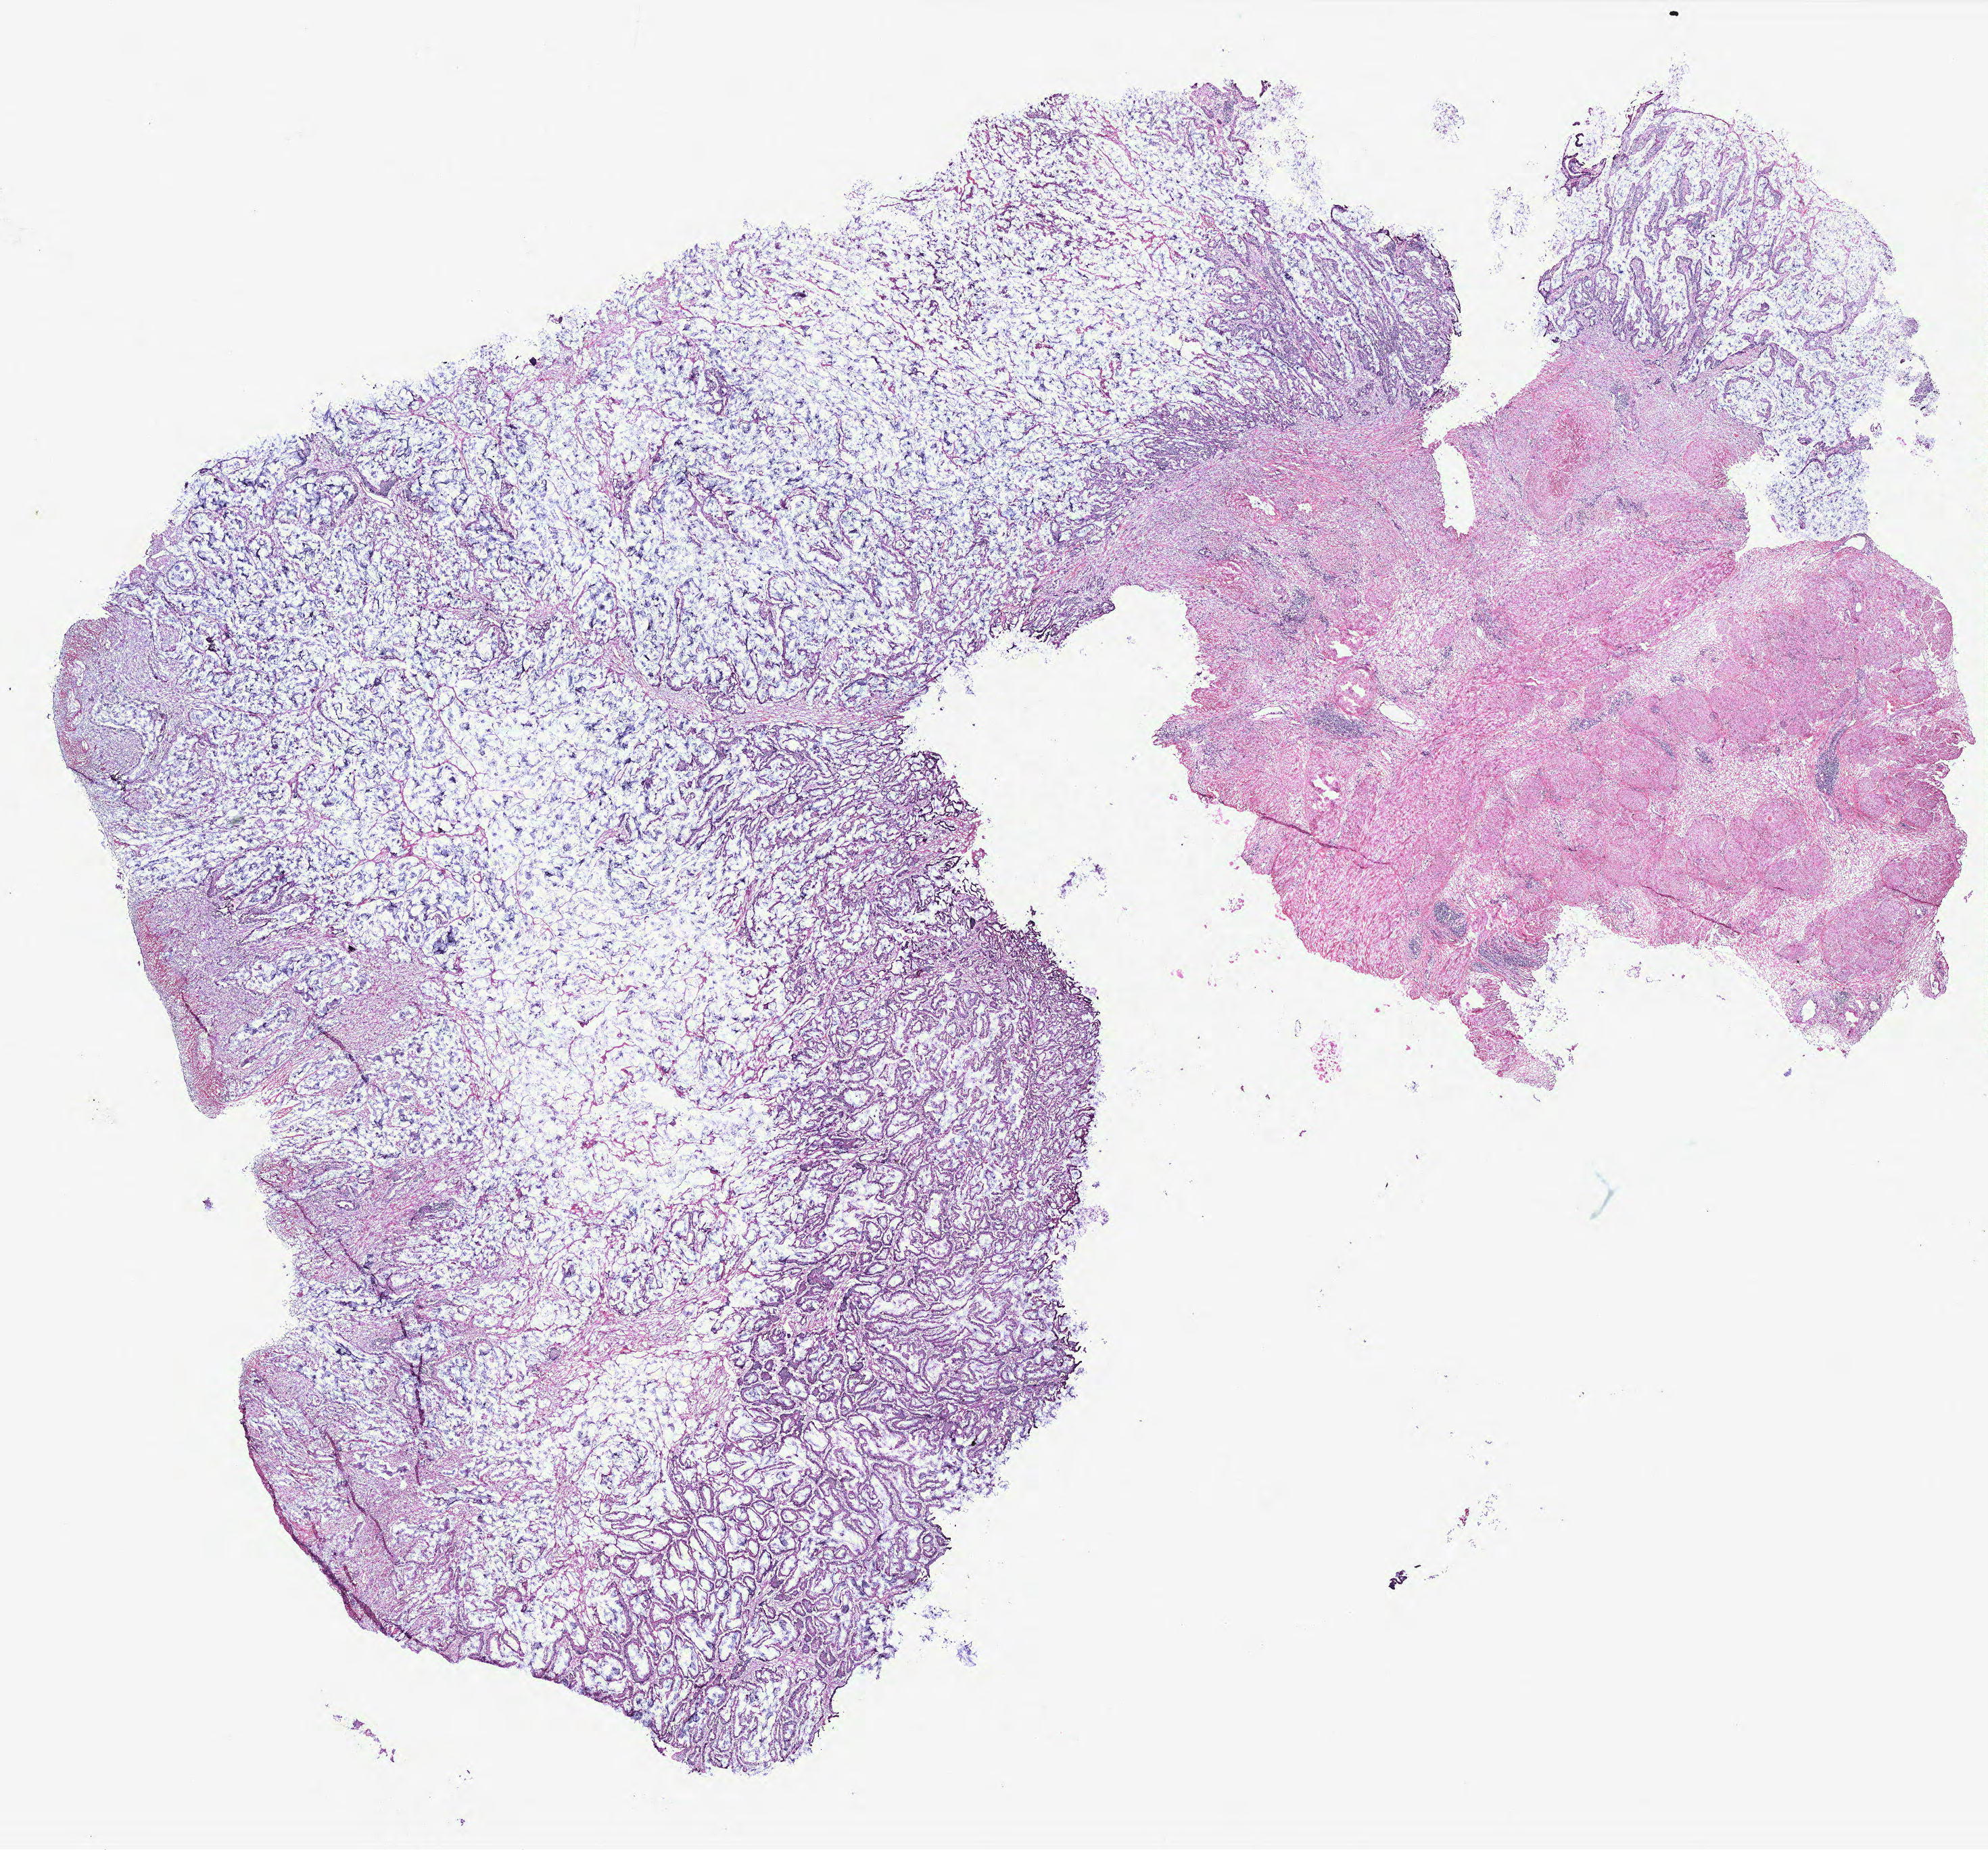
Digitized H&E-stained tissue section (whole slide) — low-resolution overview of the scanned area, about 23.5 x 21.9 mm (slide scanned at 40x), colon, tissue type not recorded.
- patient diagnosis (cohort enrolment): colon cancer (colon)